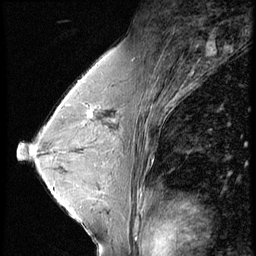
Breast MRI (dynamic contrast-enhanced), one sagittal slice. Slice 37 of 56 in the series (ordered by position). 4 images stored at this slice position (order not interpretable as contrast timing). 1.5 T. TE 4.2 ms, TR 9 ms. 2.5 mm slice thickness. 256 × 256 image matrix. Female patient, age 45 years. Case-level facts recorded for this patient, not image findings: setting: breast cancer imaged before/during neoadjuvant chemotherapy; receptor status: triple-negative.
Structures marked on this image (semi-automatic segmentation, software-assisted and operator-edited):
- analysis volume of interest (the breast-tissue region the enhancement analysis was run in; not a lesion): bounding box <77,104,97,124> (left, top, right, bottom; pixels)
- tumour enhancement mask (voxels above the 140 % enhancement threshold inside the analysis volume of interest): <77,104,97,124>